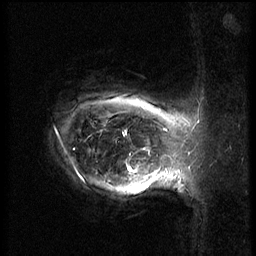
Breast MRI (dynamic contrast-enhanced), one sagittal slice. Position 53 of 62 along the scan axis. 3 images stored at this slice position (order not interpretable as contrast timing). 1.5 T. TE 4.2 ms, TR 8.9 ms. 256 × 256 image matrix, field of view 200 × 200 mm. Patient: female, 37 years. Case-level facts recorded for this patient, not image findings: setting: breast cancer imaged before/during neoadjuvant chemotherapy; receptor status: triple-negative.
Annotated regions visible in this slice (semi-automatic segmentation, software-assisted and operator-edited):
- analysis volume of interest (the breast-tissue region the enhancement analysis was run in; not a lesion): bounding box [x1, y1, x2, y2] px = [116, 146, 168, 201]
- tumour enhancement mask (voxels above the 140 % enhancement threshold inside the analysis volume of interest): [128, 168, 130, 171]